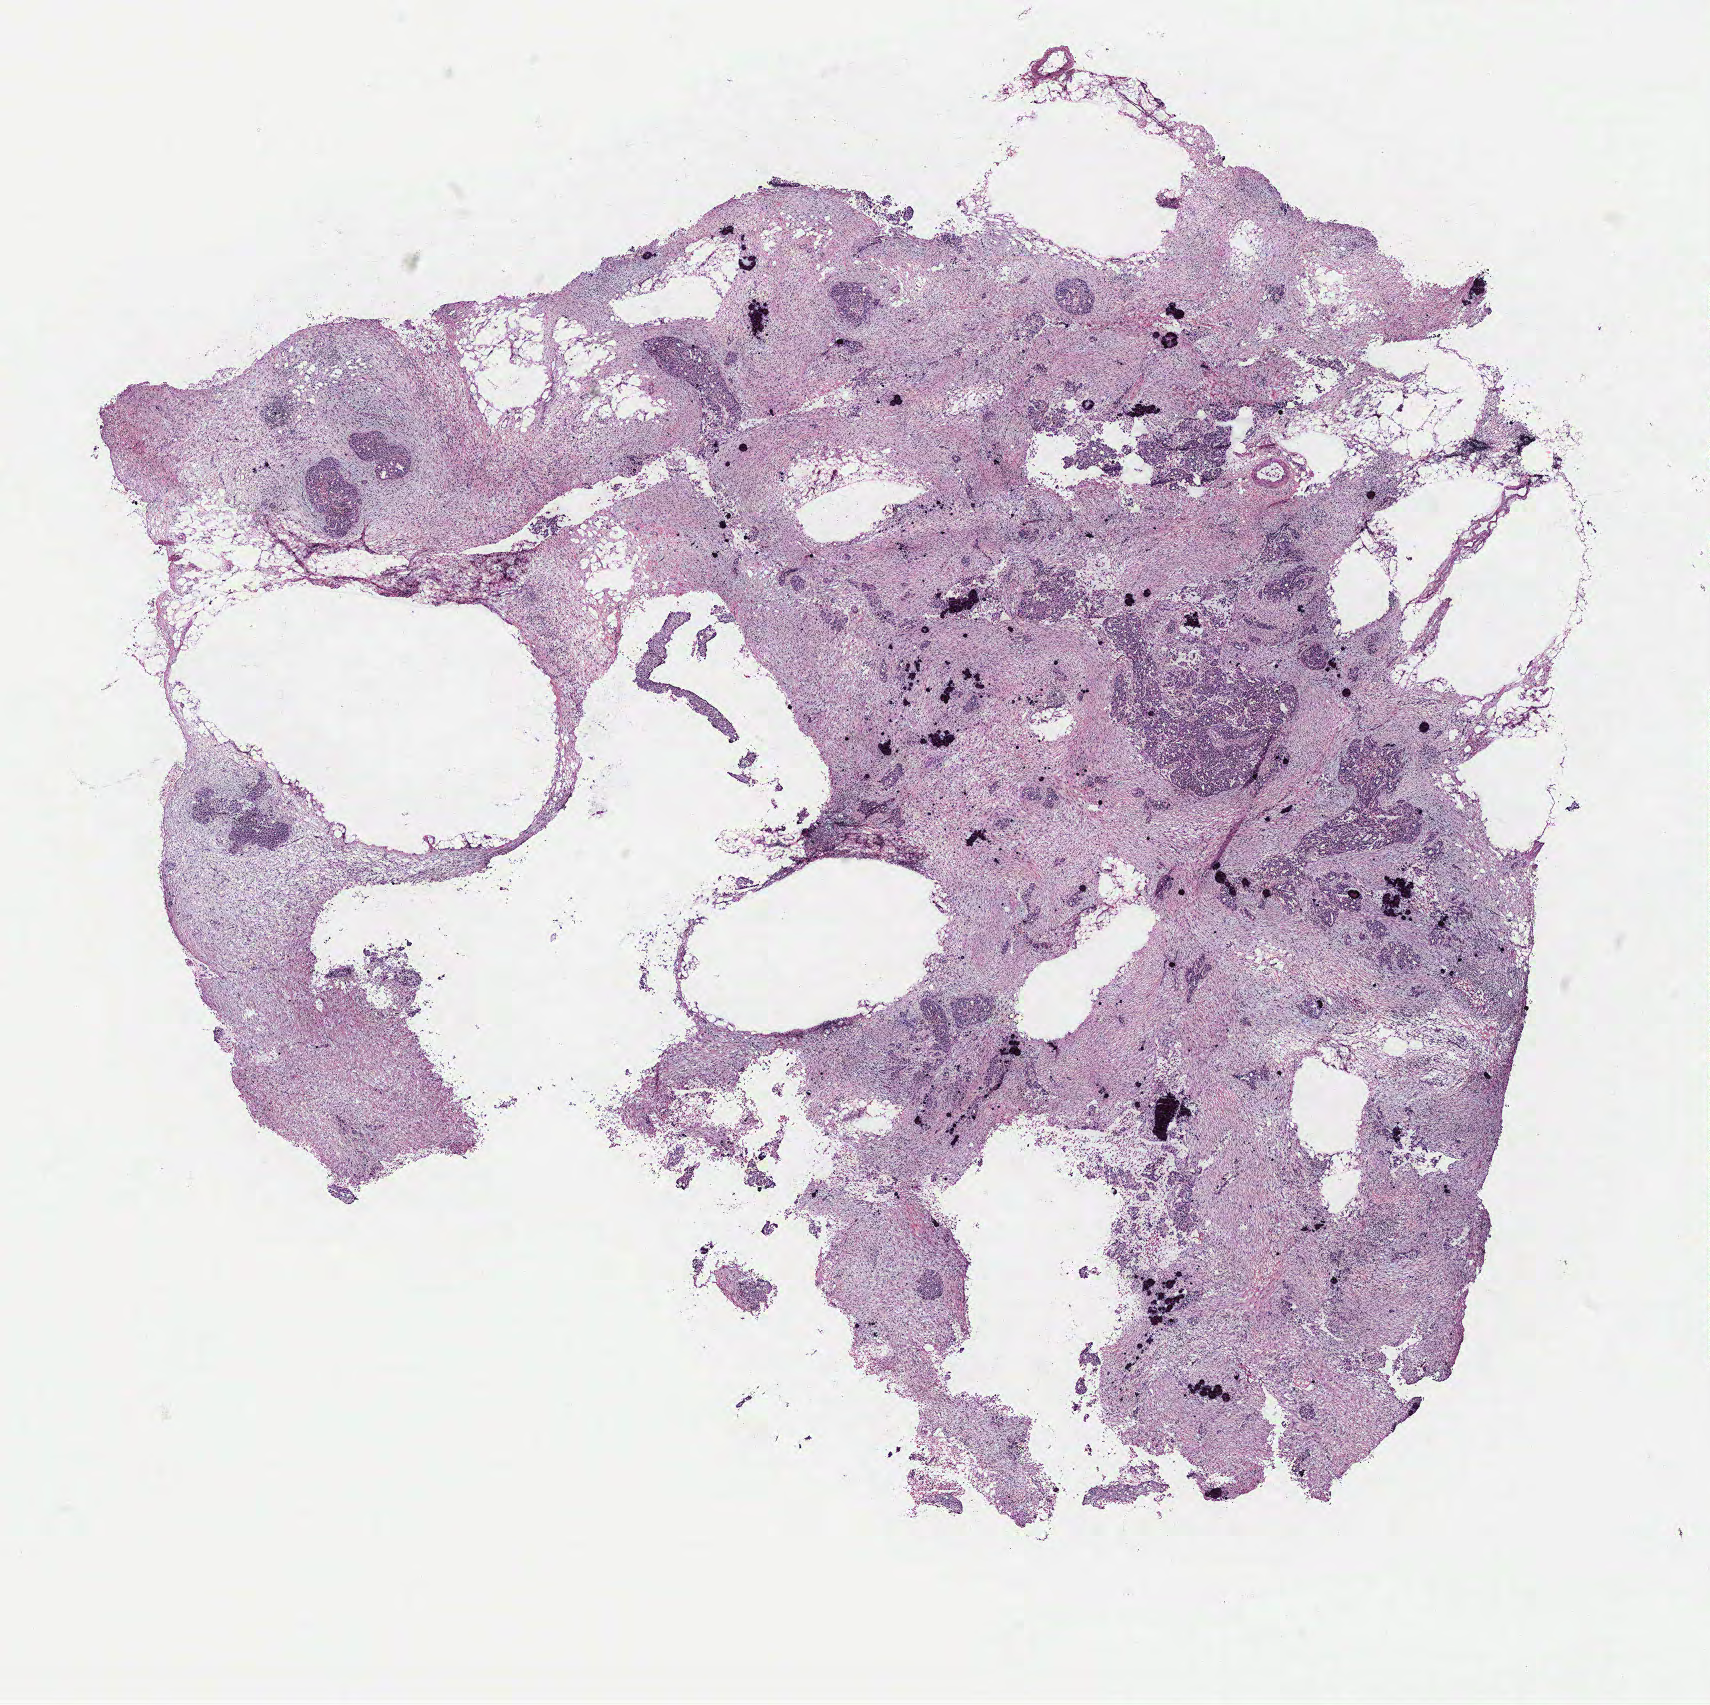
Digitized Hematoxylin and eosin (H&E) stained tissue section (whole slide) — shown as a low-resolution overview of the whole scanned area (about 13.7 x 13.6 mm). Tumour tissue sample, ovary. 53-year-old female patient.
Primary tumour site (as recorded): fallopian tube. Histologic diagnosis: Serous adenocarcinoma, NOS (fallopian tube).